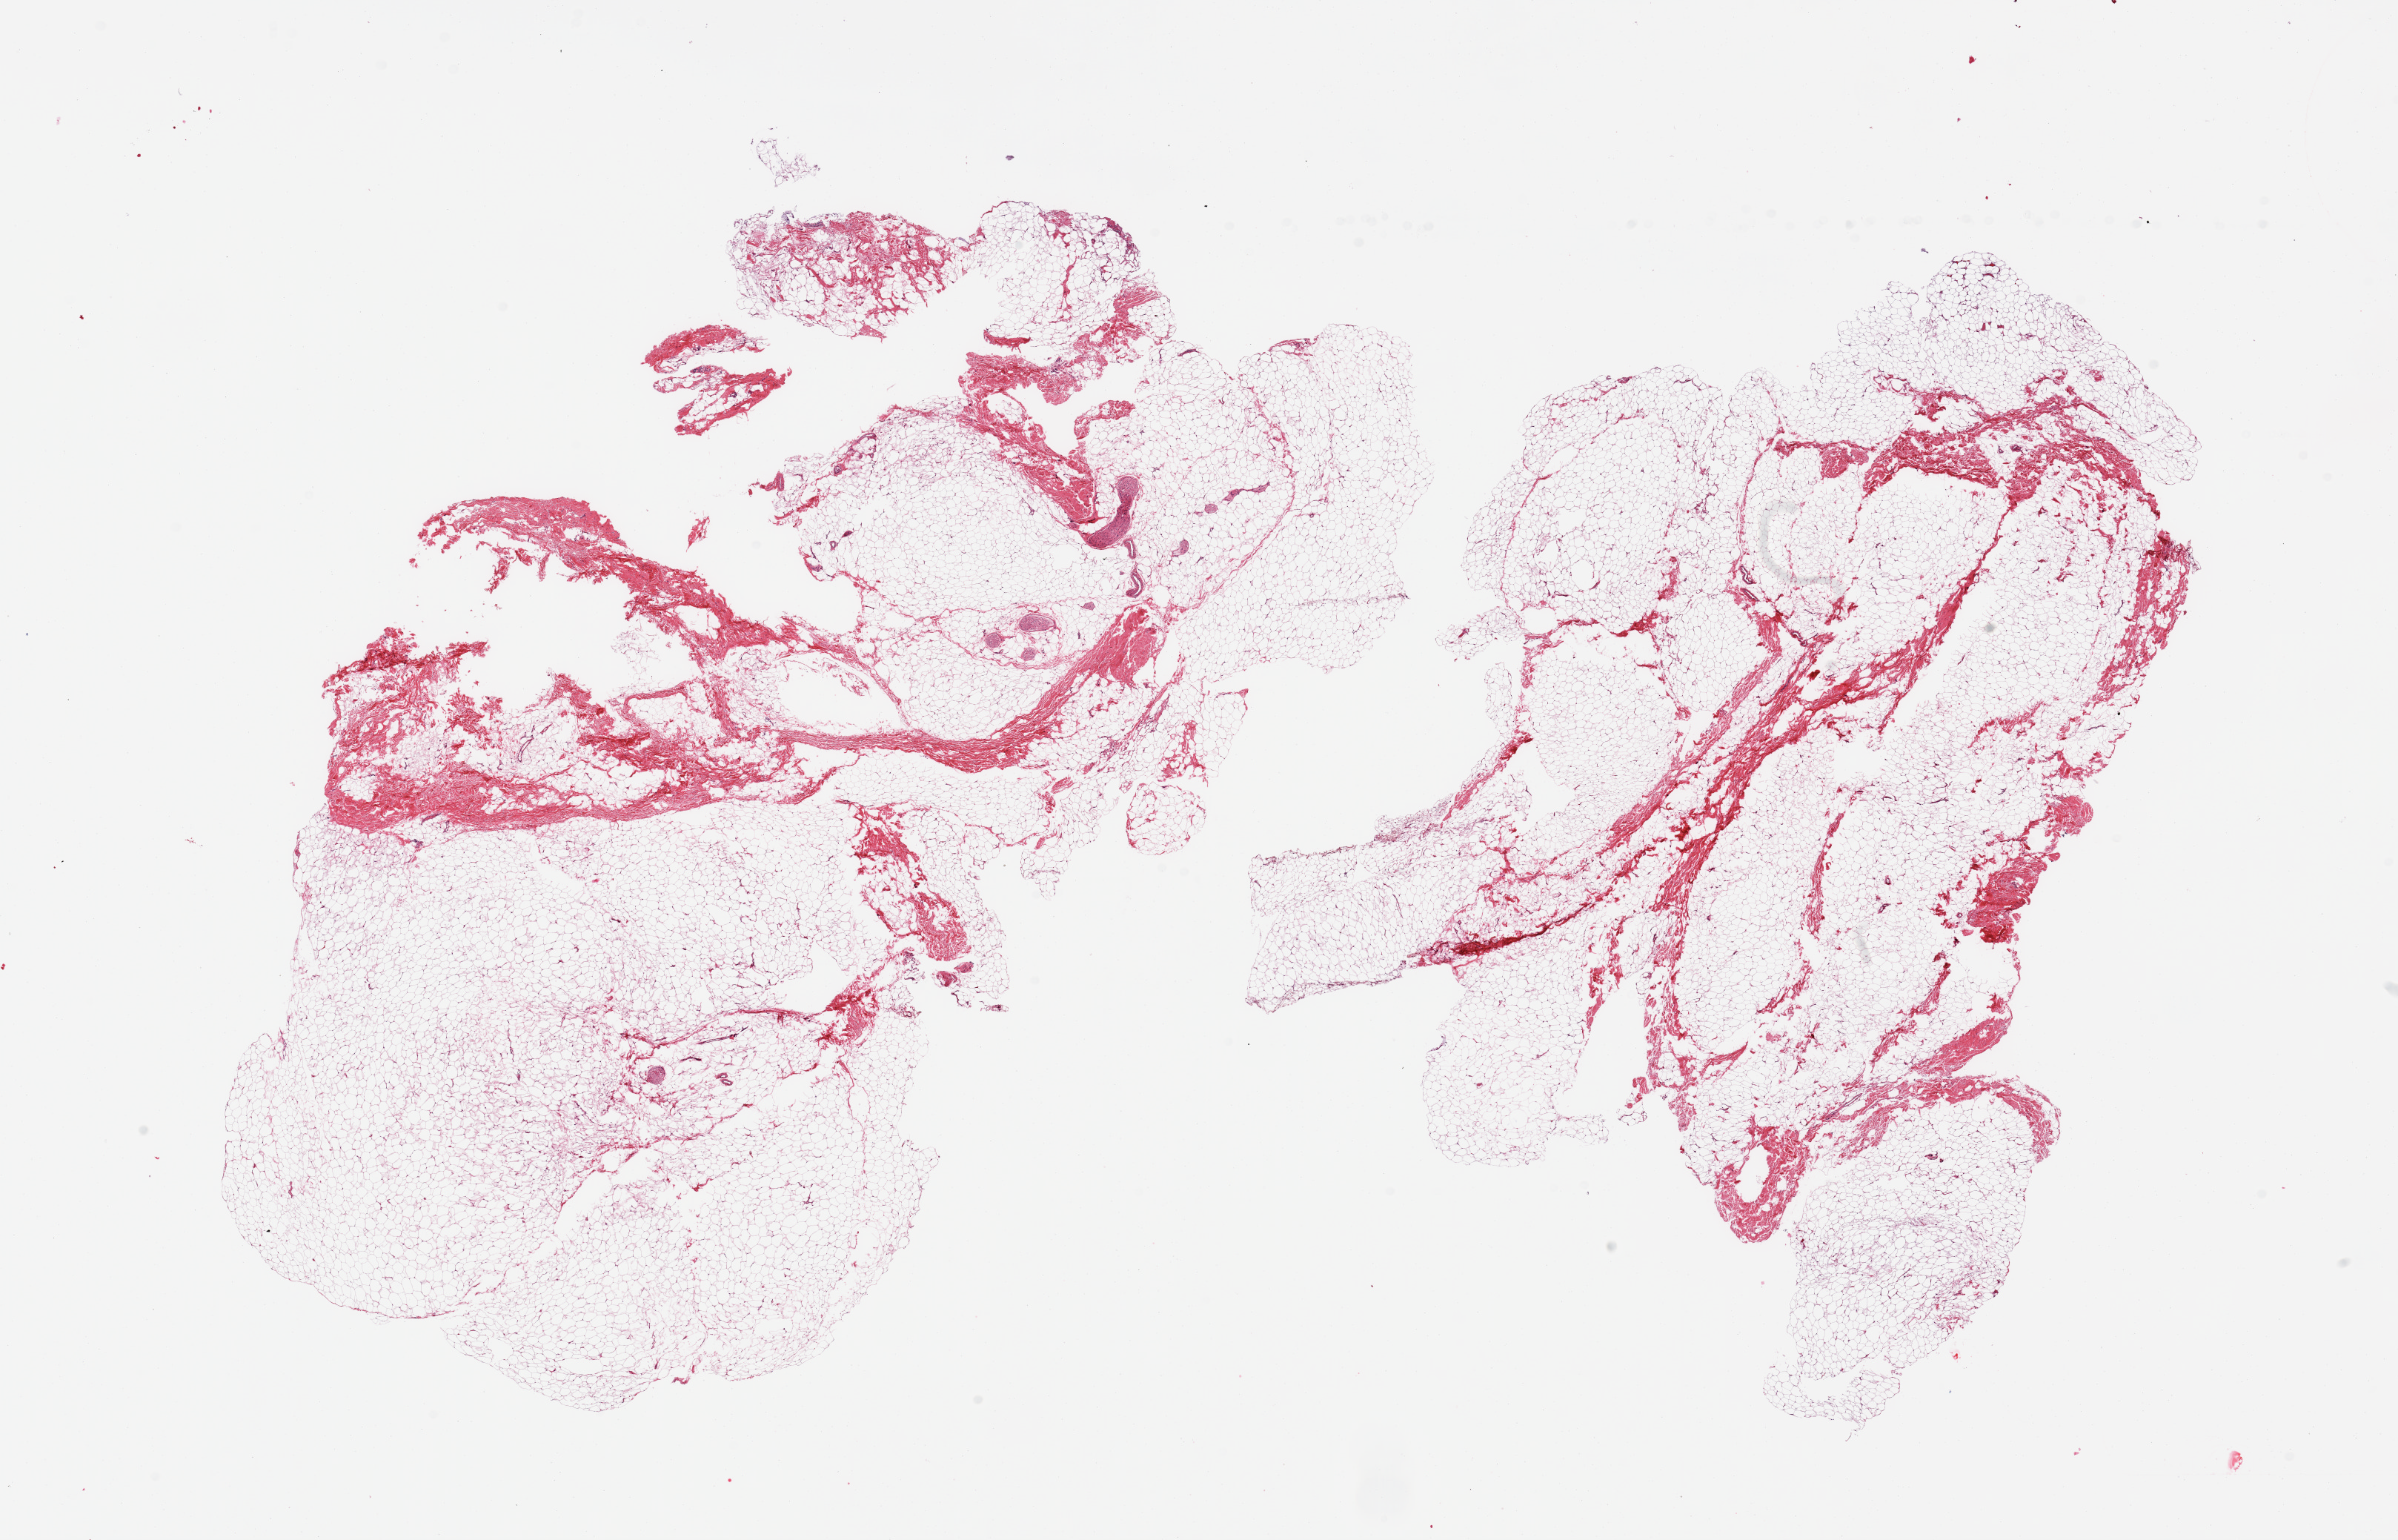
Hematoxylin and eosin (H&E) whole-slide image, brightfield, whole scanned area (about 25.6 x 16.4 mm) shown as a low-resolution overview; PAXgene-fixed paraffin-embedded (PFPE) section; target tissue: breast; tissue donor sample. Male donor.
* pathologist's review note for this sample: 2 pieces; 80-90% fat with some fibrous stroma/nerves